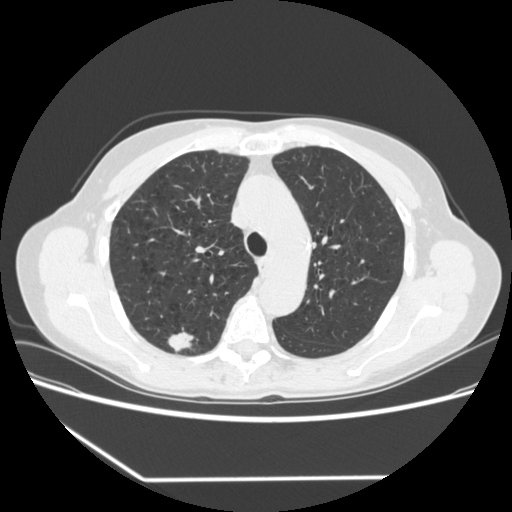
Low-dose screening chest CT, one axial slice; slice 243 of 323 in the series (ordered by position); reconstruction kernel STANDARD; 120 kVp; lung window (W 1500 / L -600 HU); 512 × 512 image matrix.
Annotated regions visible in this slice (manually delineated by an expert):
- lesion 1 (tumor, upper lobe of right lung): bounding box <168,327,198,353> (left, top, right, bottom; pixels)